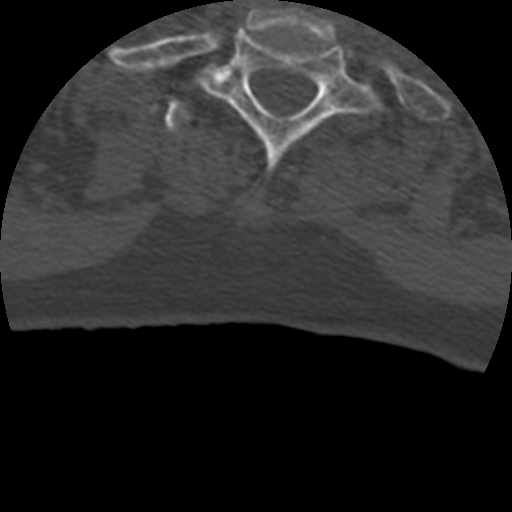
CT including the spine, one axial slice; position 384 of 399 along the scan axis; bone window (W 1800 / L 400 HU); 512 × 512 image matrix, field of view 160 × 160 mm. Patient age 69 years. Case-level facts recorded for this patient, not image findings: primary cancer: prostate.
Structures marked on this image (semi-automatic segmentation, software-assisted and operator-edited):
- T1 vertebra: bounding box (x1, y1, x2, y2) in pixels: (202, 29, 378, 183)
- T2 vertebra: (165, 100, 386, 152)